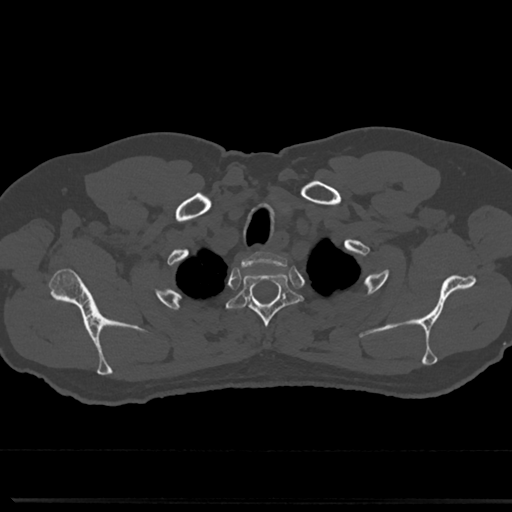
CT including the spine, one axial slice; slice 640 of 817 in the series (ordered by position); 120 kVp; bone window (W 1800 / L 400 HU); 512 × 512 image matrix. Patient: male, 61 years. Case-level facts recorded for this patient, not image findings: primary cancer: prostate.
Structures marked on this image (semi-automatically segmented with operator editing):
- T1 vertebra: bounding box [x1, y1, x2, y2] px = [254, 253, 260, 257]
- T2 vertebra: [230, 266, 297, 352]